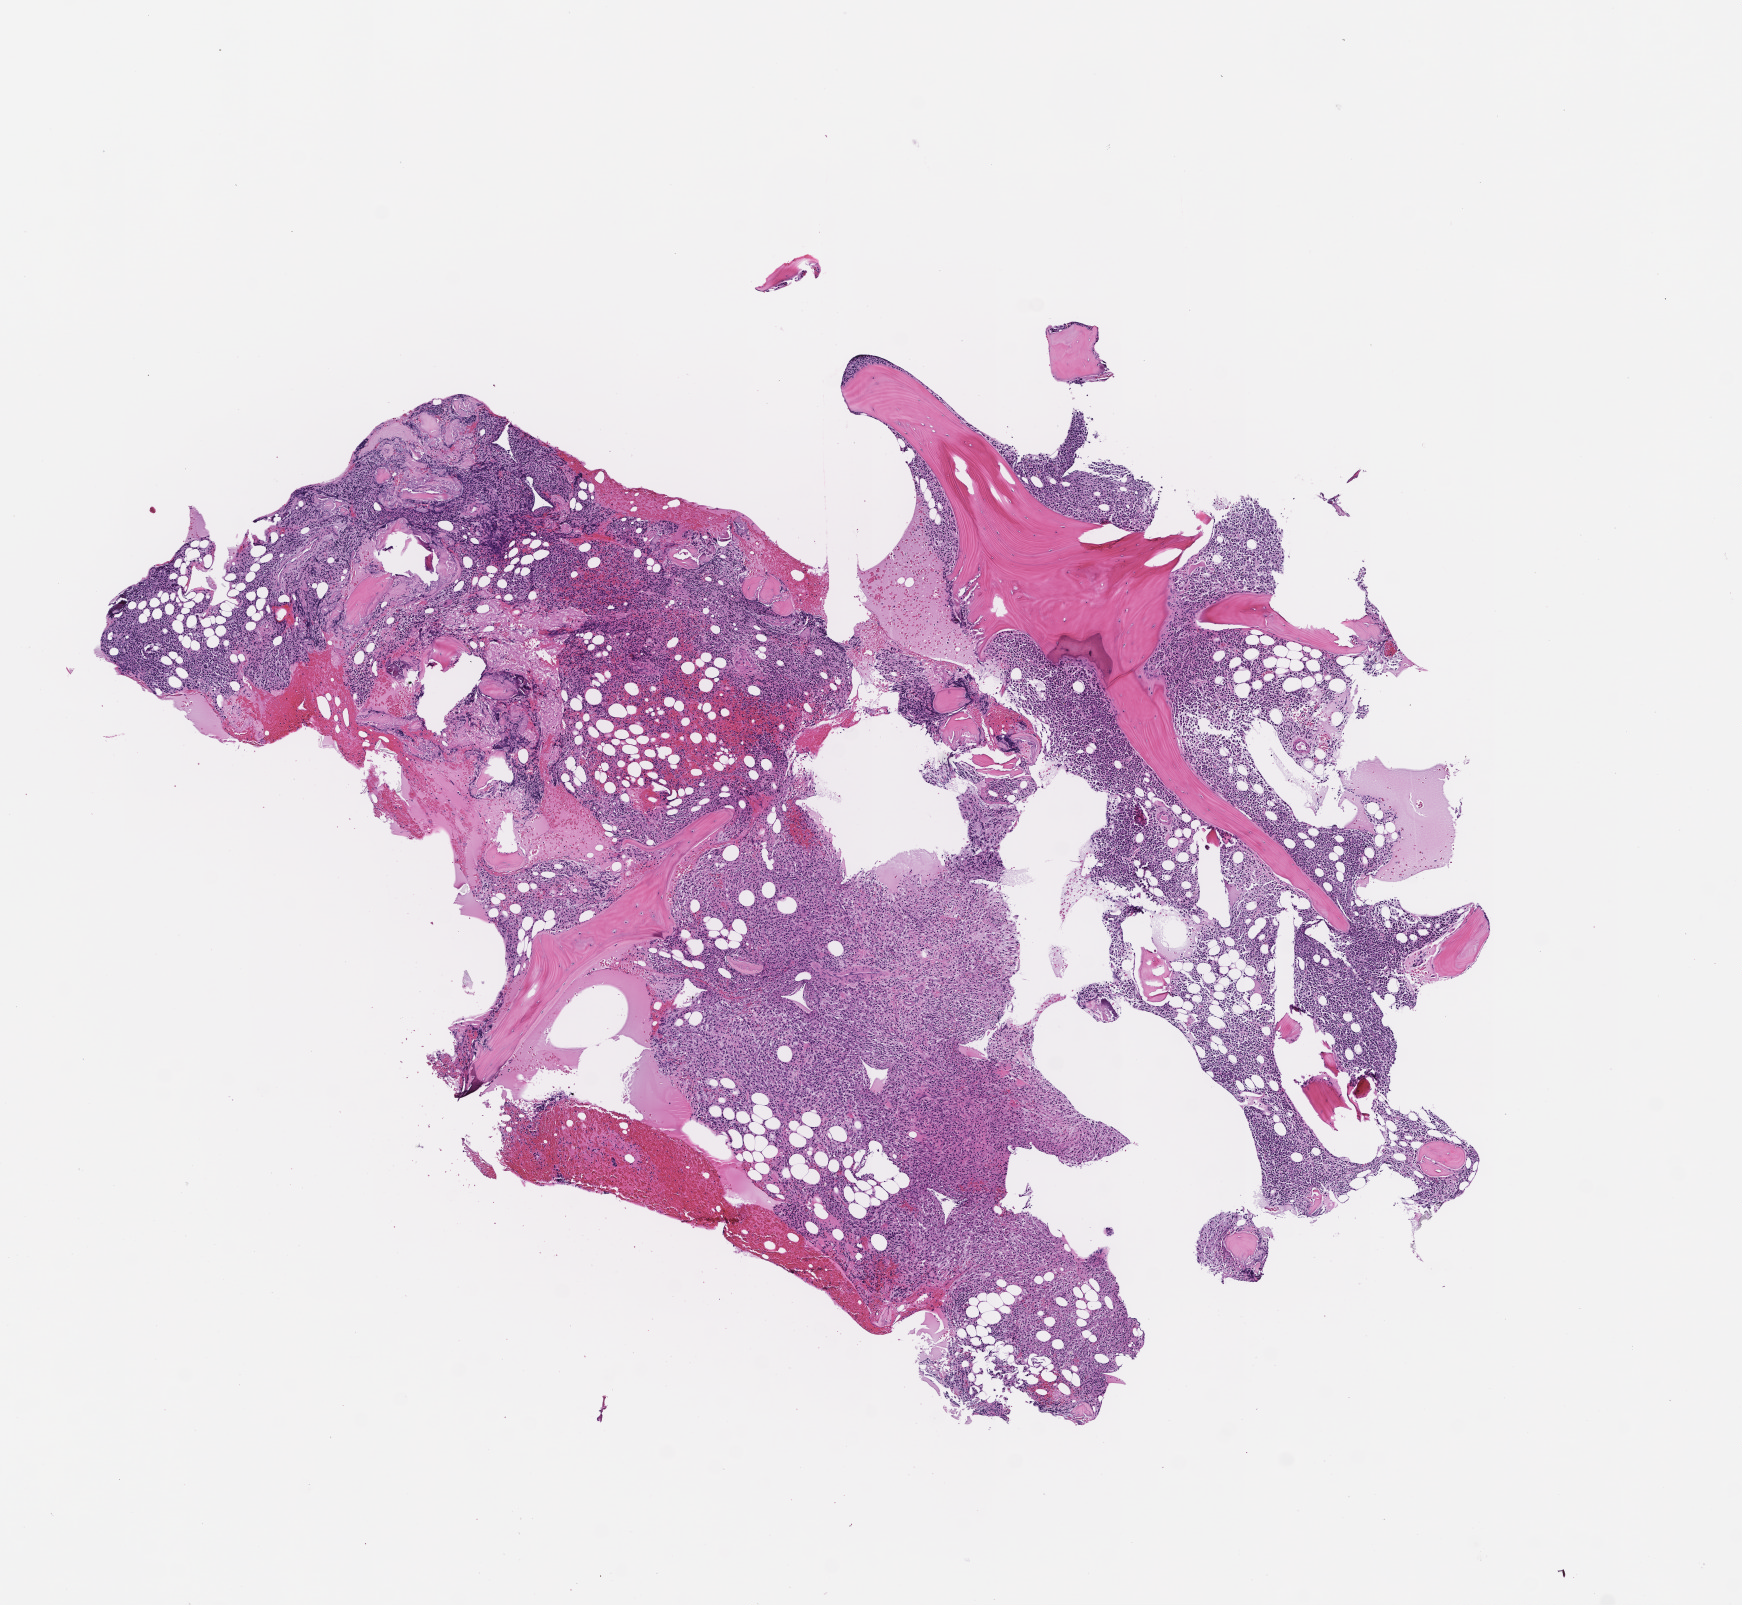
Whole-slide image, H&E stain — shown as a low-resolution overview of the whole scanned area (about 7.0 x 6.5 mm). Formalin-fixed paraffin-embedded section. Site: bone marrow. Specimen time point: collected at disease progression. Patient sex: female.
* this section: primary tumour tissue
* diagnosis: Plasma Cell Myeloma